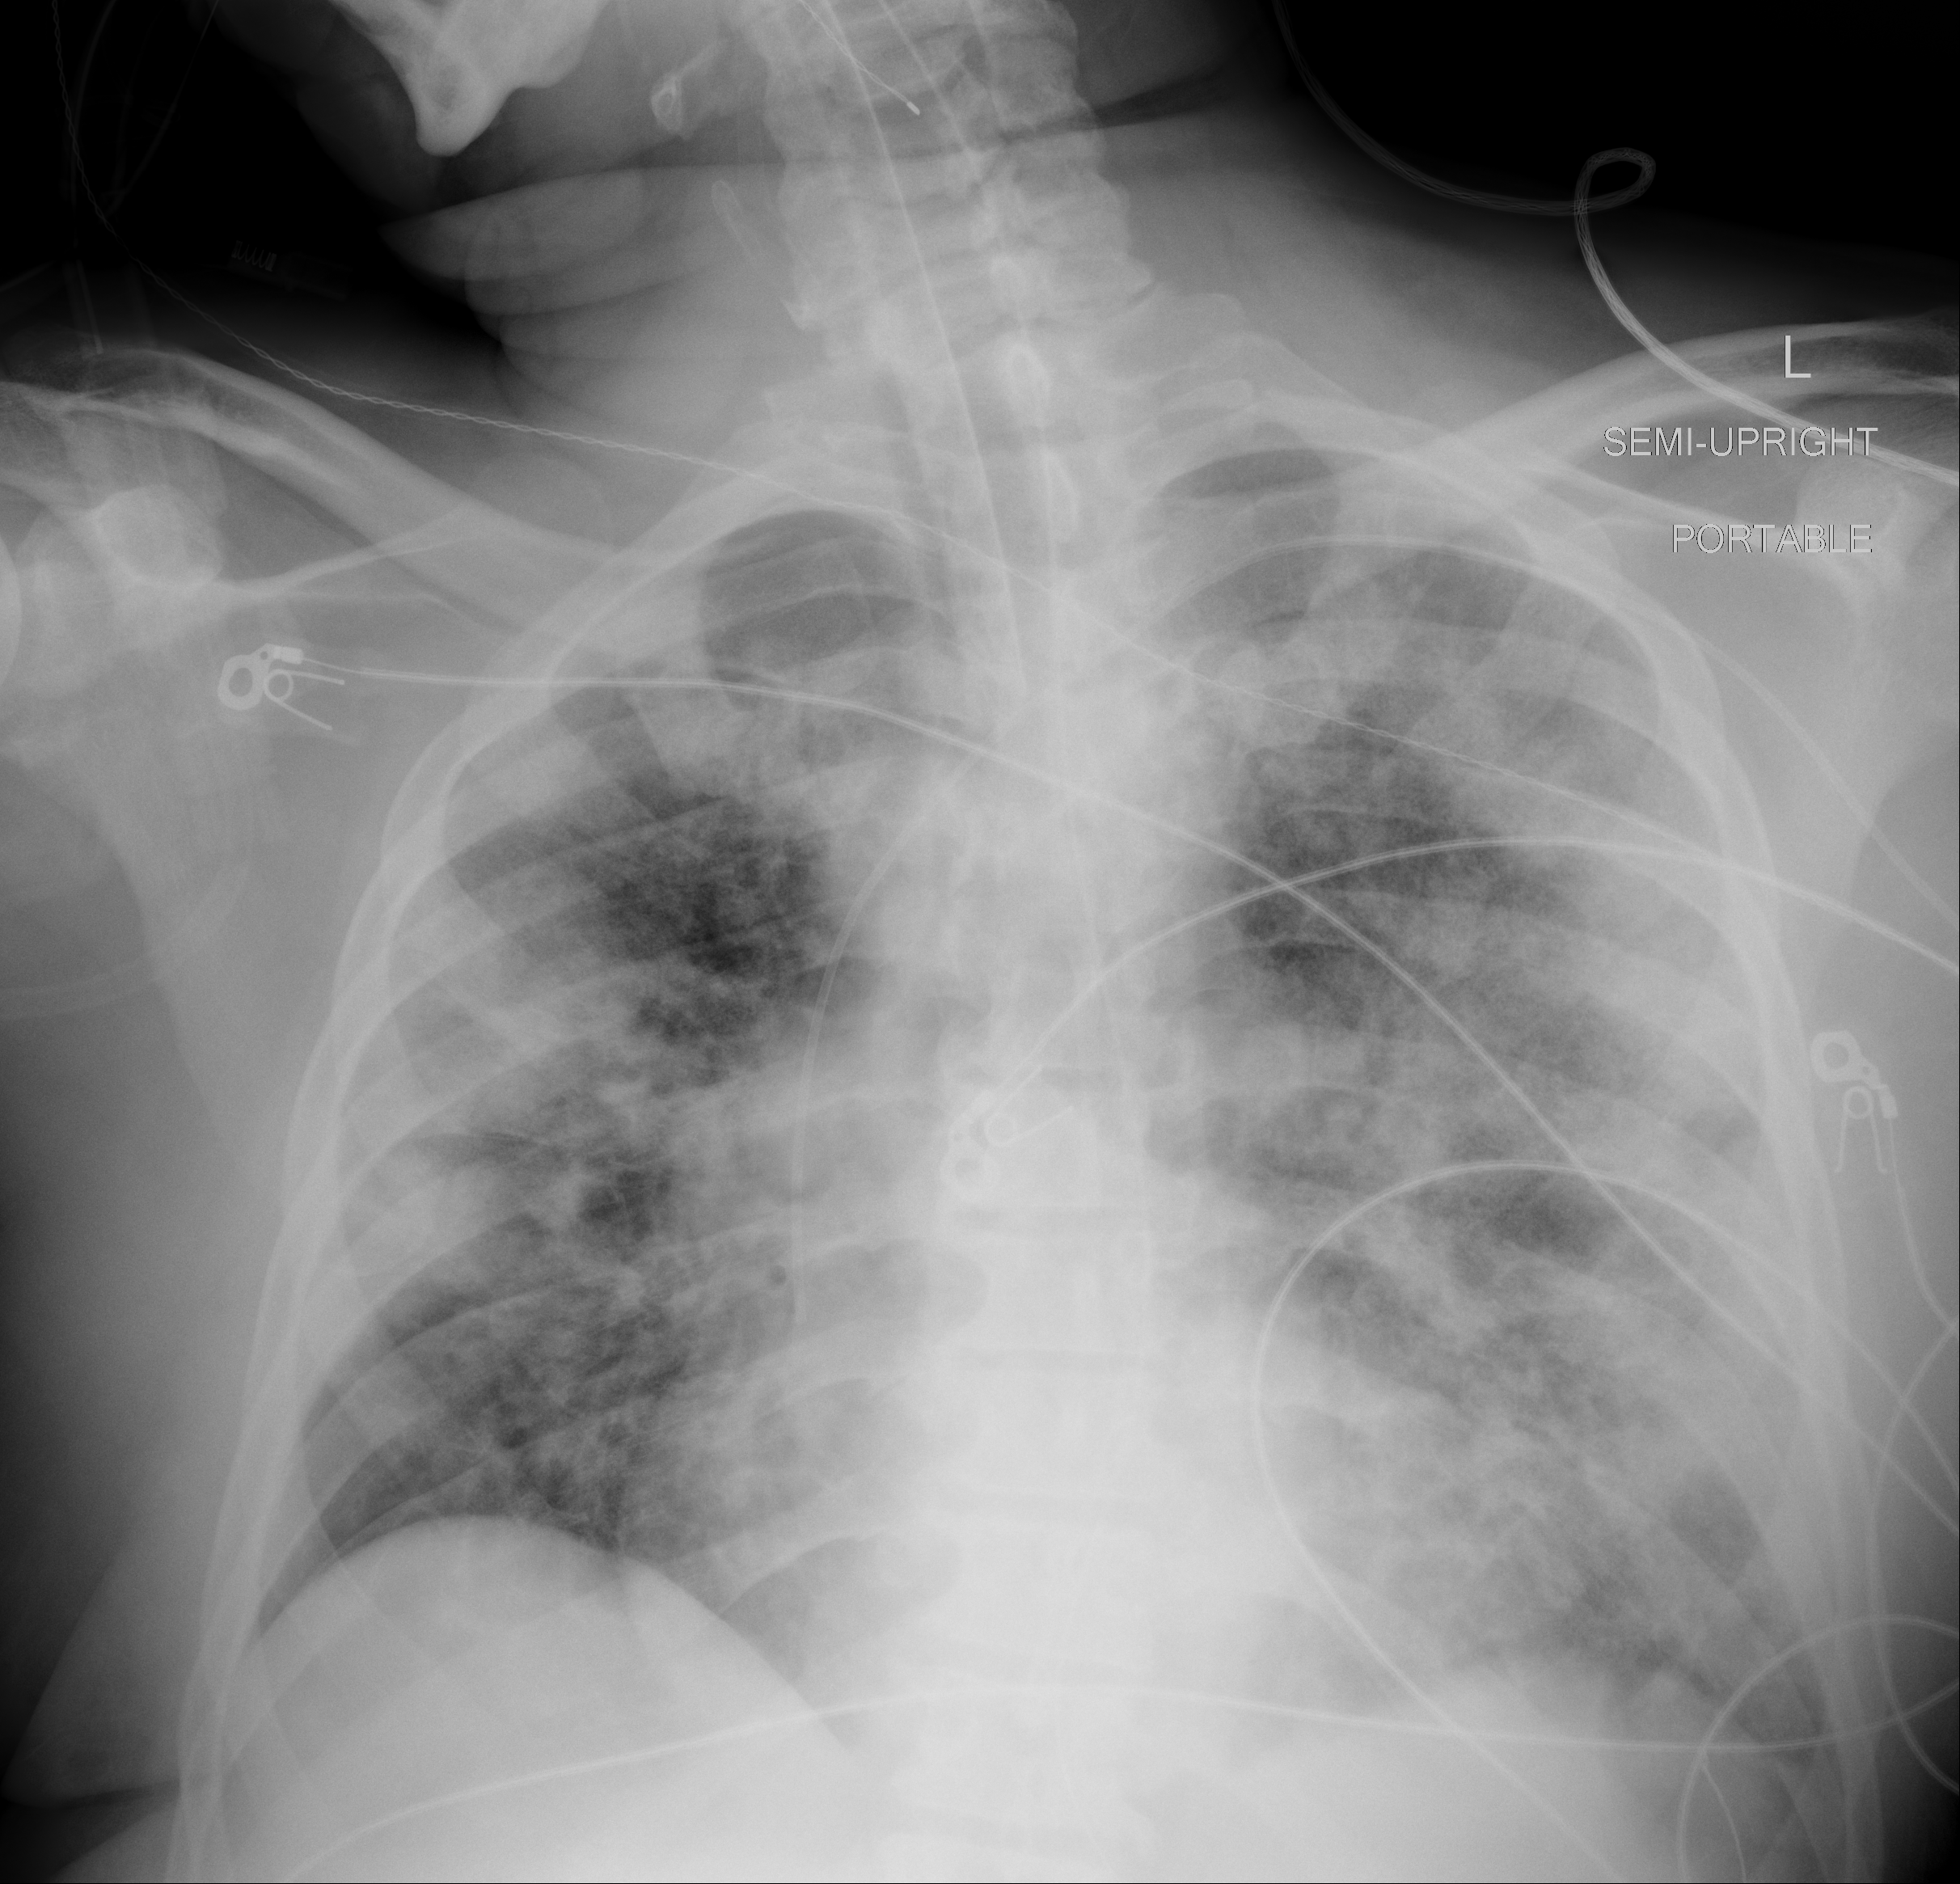
Portable chest radiograph, AP projection. Male patient, age 64 years; imaged 4 days after the COVID-19 diagnosis.
Radiologist key findings (as recorded): Significant worsening in multifocal infection involving both lung.